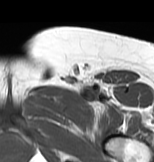
MRI of an extremity soft-tissue mass, one axial slice. Position 53 of 83 along the scan axis. MR volume resampled by the dataset authors to the PET/CT grid (not the native acquisition matrix). 3.27 mm slice thickness. 154 × 162 image matrix, field of view 150 × 158 mm. Female patient. Case-level facts recorded for this patient, not image findings: histological type: myxofibrosarcoma; grade: intermediate; site of the primary tumour: left thigh.
Outlined on this slice (expert contour drawn on MRI and transferred to this co-registered scan by the dataset authors):
- gross tumour volume including surrounding oedema: bounding box (x1, y1, x2, y2) in pixels: (30, 86, 116, 117)